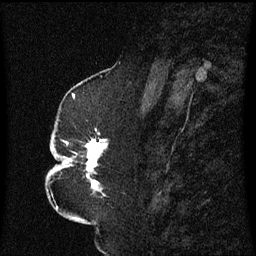
Breast MRI (dynamic contrast-enhanced), one sagittal slice. Slice 27 of 60 in the series (ordered by position). Dynamic contrast-enhanced series, image 2 of 3 at this slice position (ordered by acquisition). 1.5 T. TE 4.2 ms, TR 8.4 ms. 2.3 mm slice thickness. 256 × 256 image matrix, field of view 200 × 200 mm. Female patient, age 52 years. Case-level facts recorded for this patient, not image findings: setting: breast cancer imaged before/during neoadjuvant chemotherapy; receptor status: HR-positive, HER2-negative.
Structures marked on this image (semi-automatically segmented with operator editing):
- analysis volume of interest (the breast-tissue region the enhancement analysis was run in; not a lesion): bounding box [x1, y1, x2, y2] px = [49, 124, 108, 197]
- tumour enhancement mask (voxels above the 70 % enhancement threshold inside the analysis volume of interest): [54, 140, 107, 189]